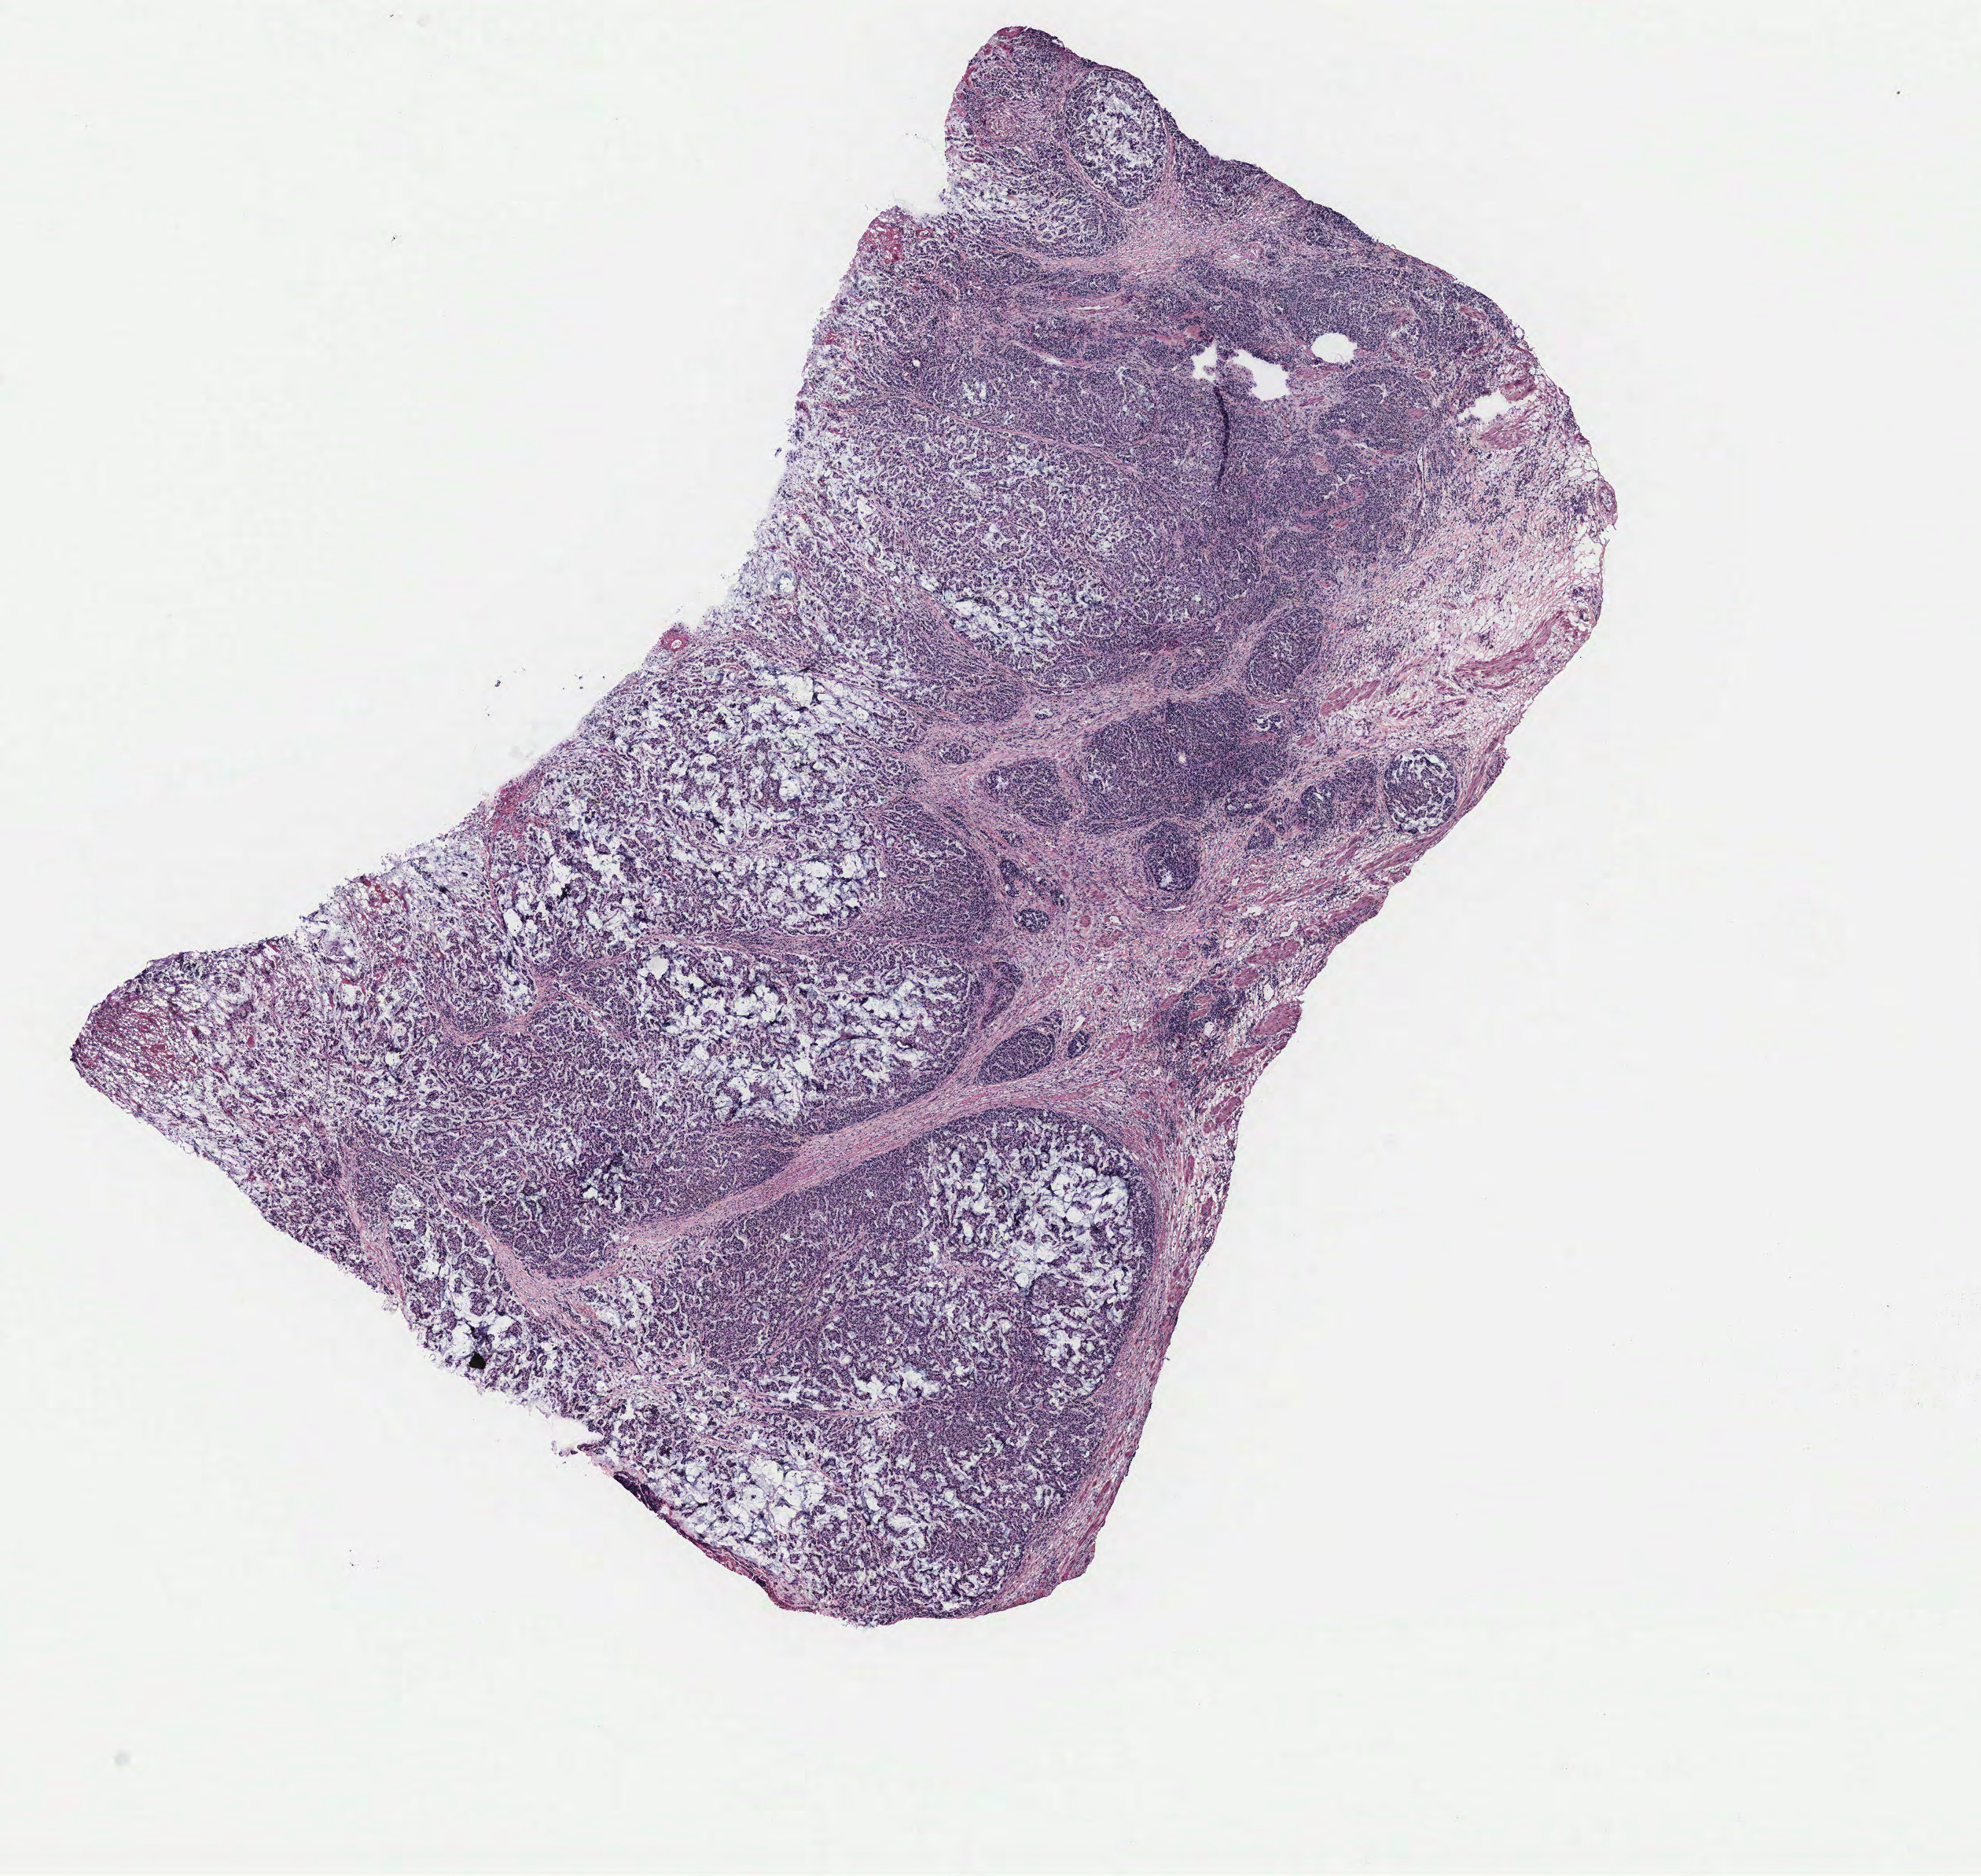
Digitized H&E-stained tissue section (whole slide) — shown as a low-resolution overview of the whole scanned area (about 10.1 x 9.6 mm, from a 40x scan), colon, normal (non-tumour) tissue. Female, 83 y/o.
• this section: normal (non-tumour) tissue from the same patient
• patient diagnosis: Adenocarcinoma, NOS